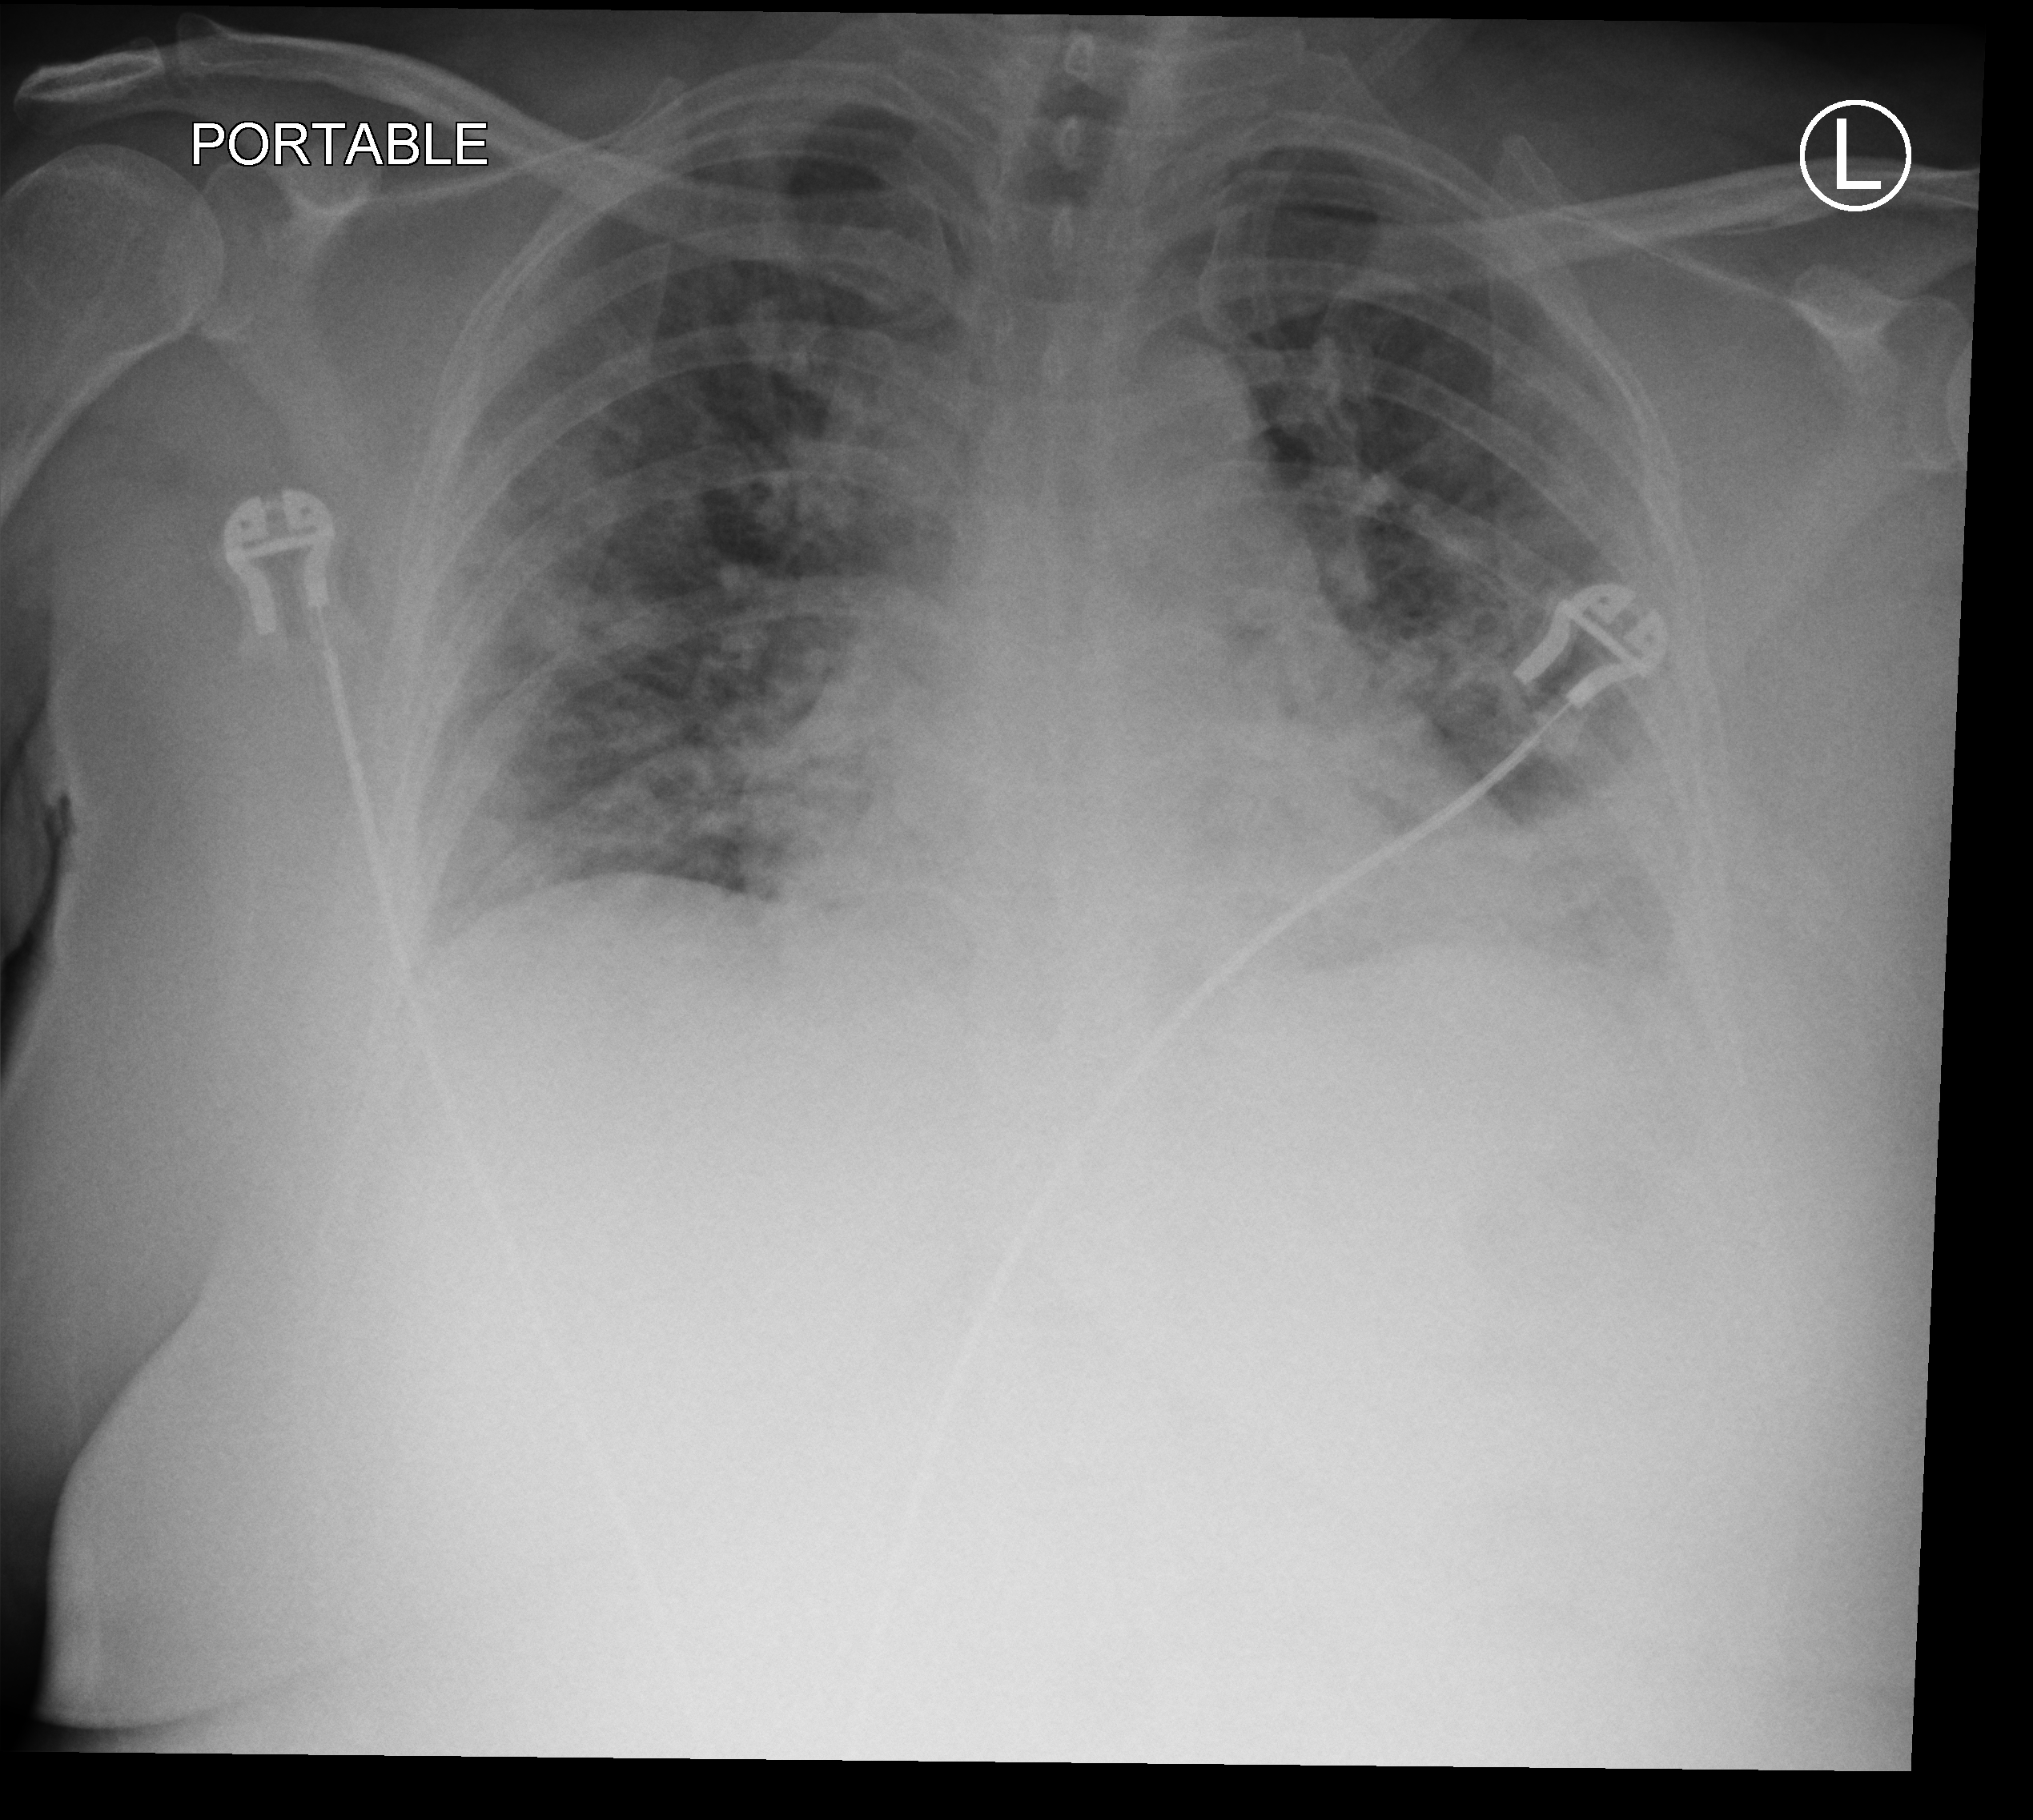
Chest X-ray (portable); anteroposterior (AP) projection. Patient hospitalised with COVID-19, aged 18–59 years.
Admission-level facts for this patient (not findings on this image; timing relative to this image not recorded):
- mechanically ventilated during this hospital stay: yes